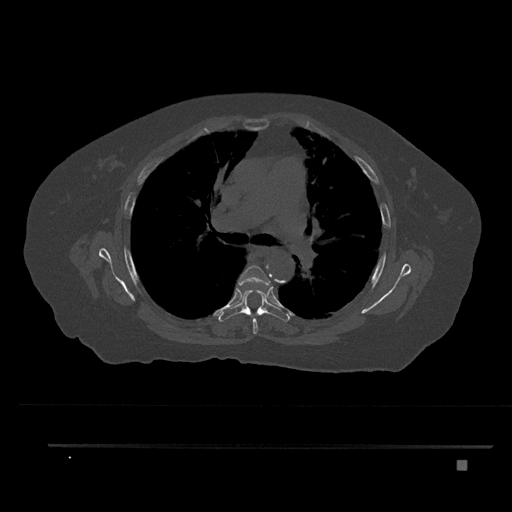
CT including the spine, one axial slice. Slice 542 of 797 in the series (ordered by position). Reconstruction kernel Br40s/3. Bone window (W 1800 / L 400 HU). 0.5 mm slice thickness. 512 × 512 image matrix. Patient: female, 76 years. Case-level facts recorded for this patient, not image findings: primary cancer: lung.
Annotated regions visible in this slice (semi-automatic segmentation, software-assisted and operator-edited):
- T5 vertebra: bounding box <238,265,271,334> (left, top, right, bottom; pixels)
- T6 vertebra: <218,290,290,322>